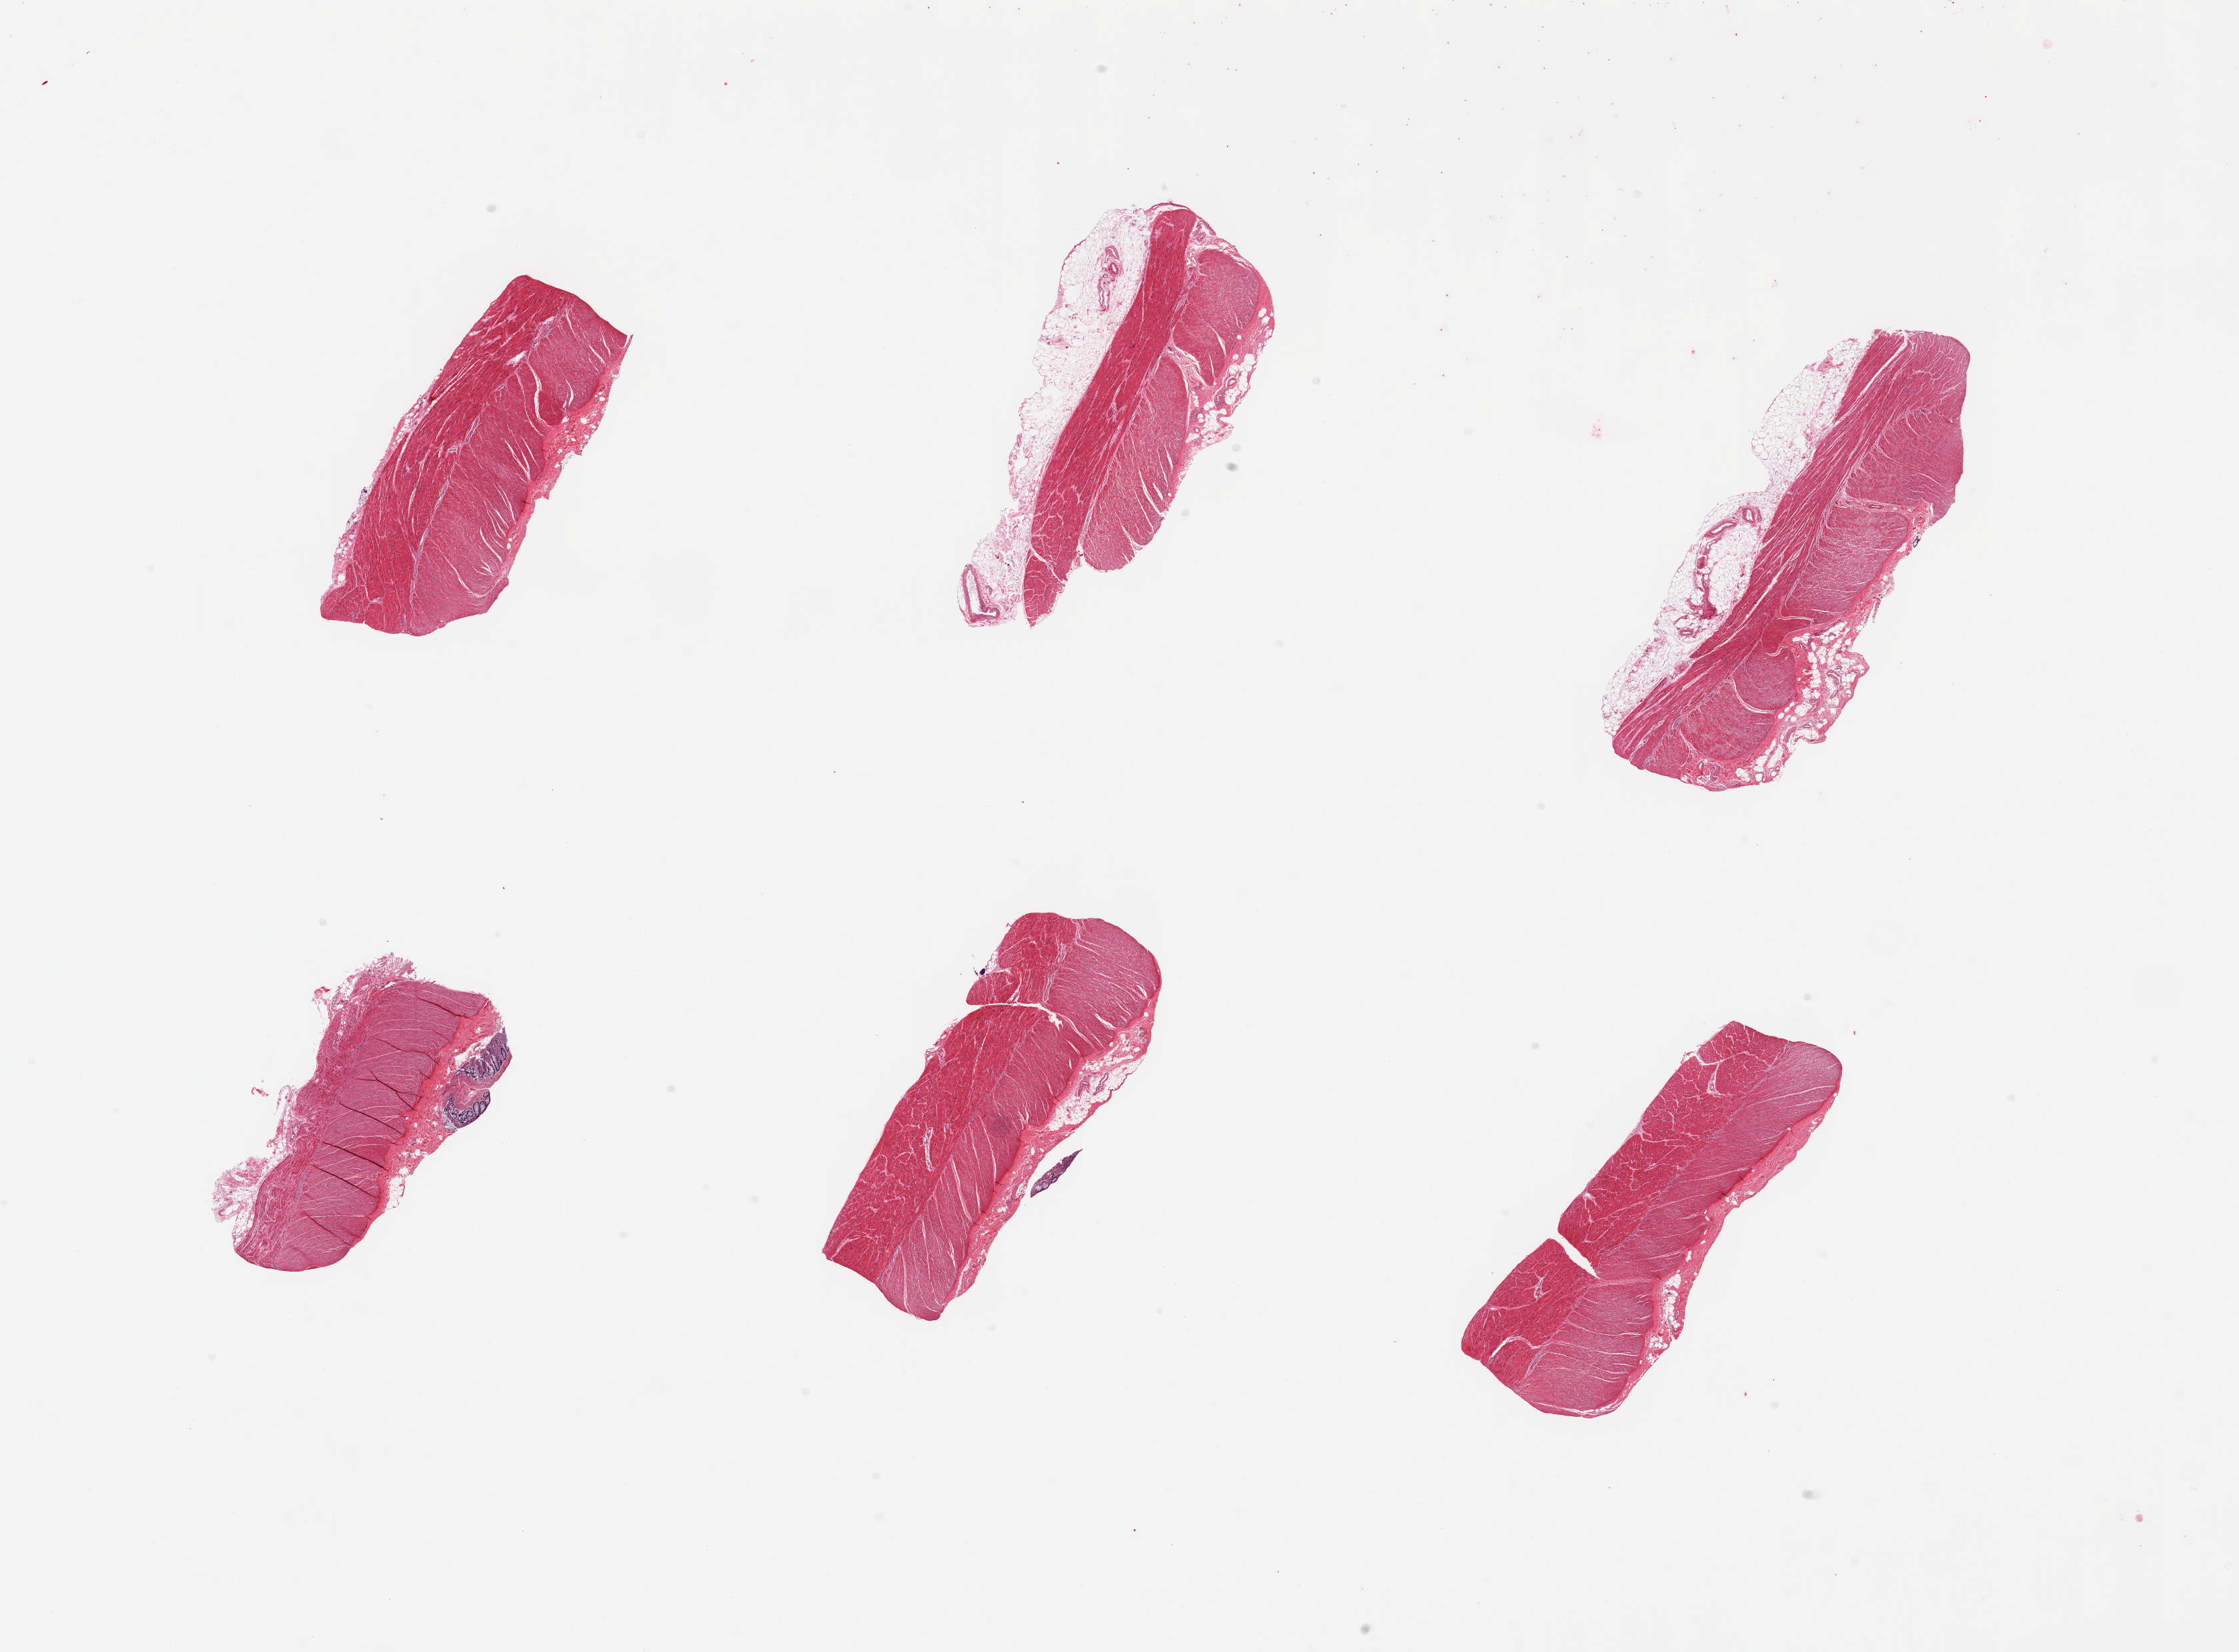
Whole-slide image, hematoxylin and eosin (H&E) stain — whole scanned area (about 26.6 x 19.6 mm, from a 20x scan) shown as a low-resolution overview, PAXgene-fixed paraffin-embedded (PFPE) section, sampled site (target tissue): sigmoid colon, tissue donor sample.
Pathologist's review note for this sample: 6 pieces; predominantly muscularis, 2 include substantial fat, 1 includes small portion of mucosa.